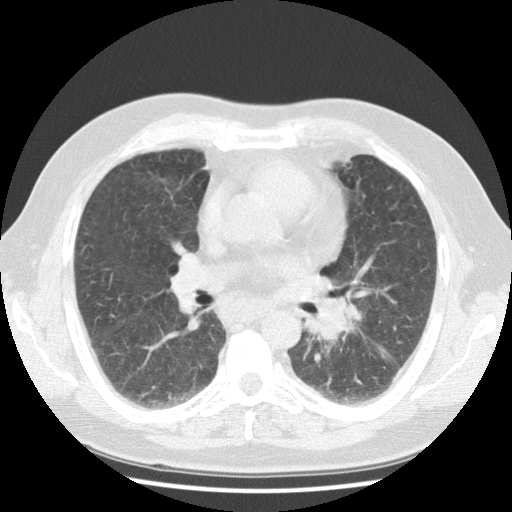
Low-dose screening chest CT, one axial slice. Position 62 of 108 along the scan axis. Reconstruction kernel STANDARD. 120 kVp. Lung window (W 1500 / L -600 HU). 512 × 512 image matrix, field of view 350 × 350 mm.
Outlined on this slice (outlined manually by an expert reader):
- lesion 1 (tumor, hilum of left lung): bounding box [x1, y1, x2, y2] px = [307, 297, 360, 339]